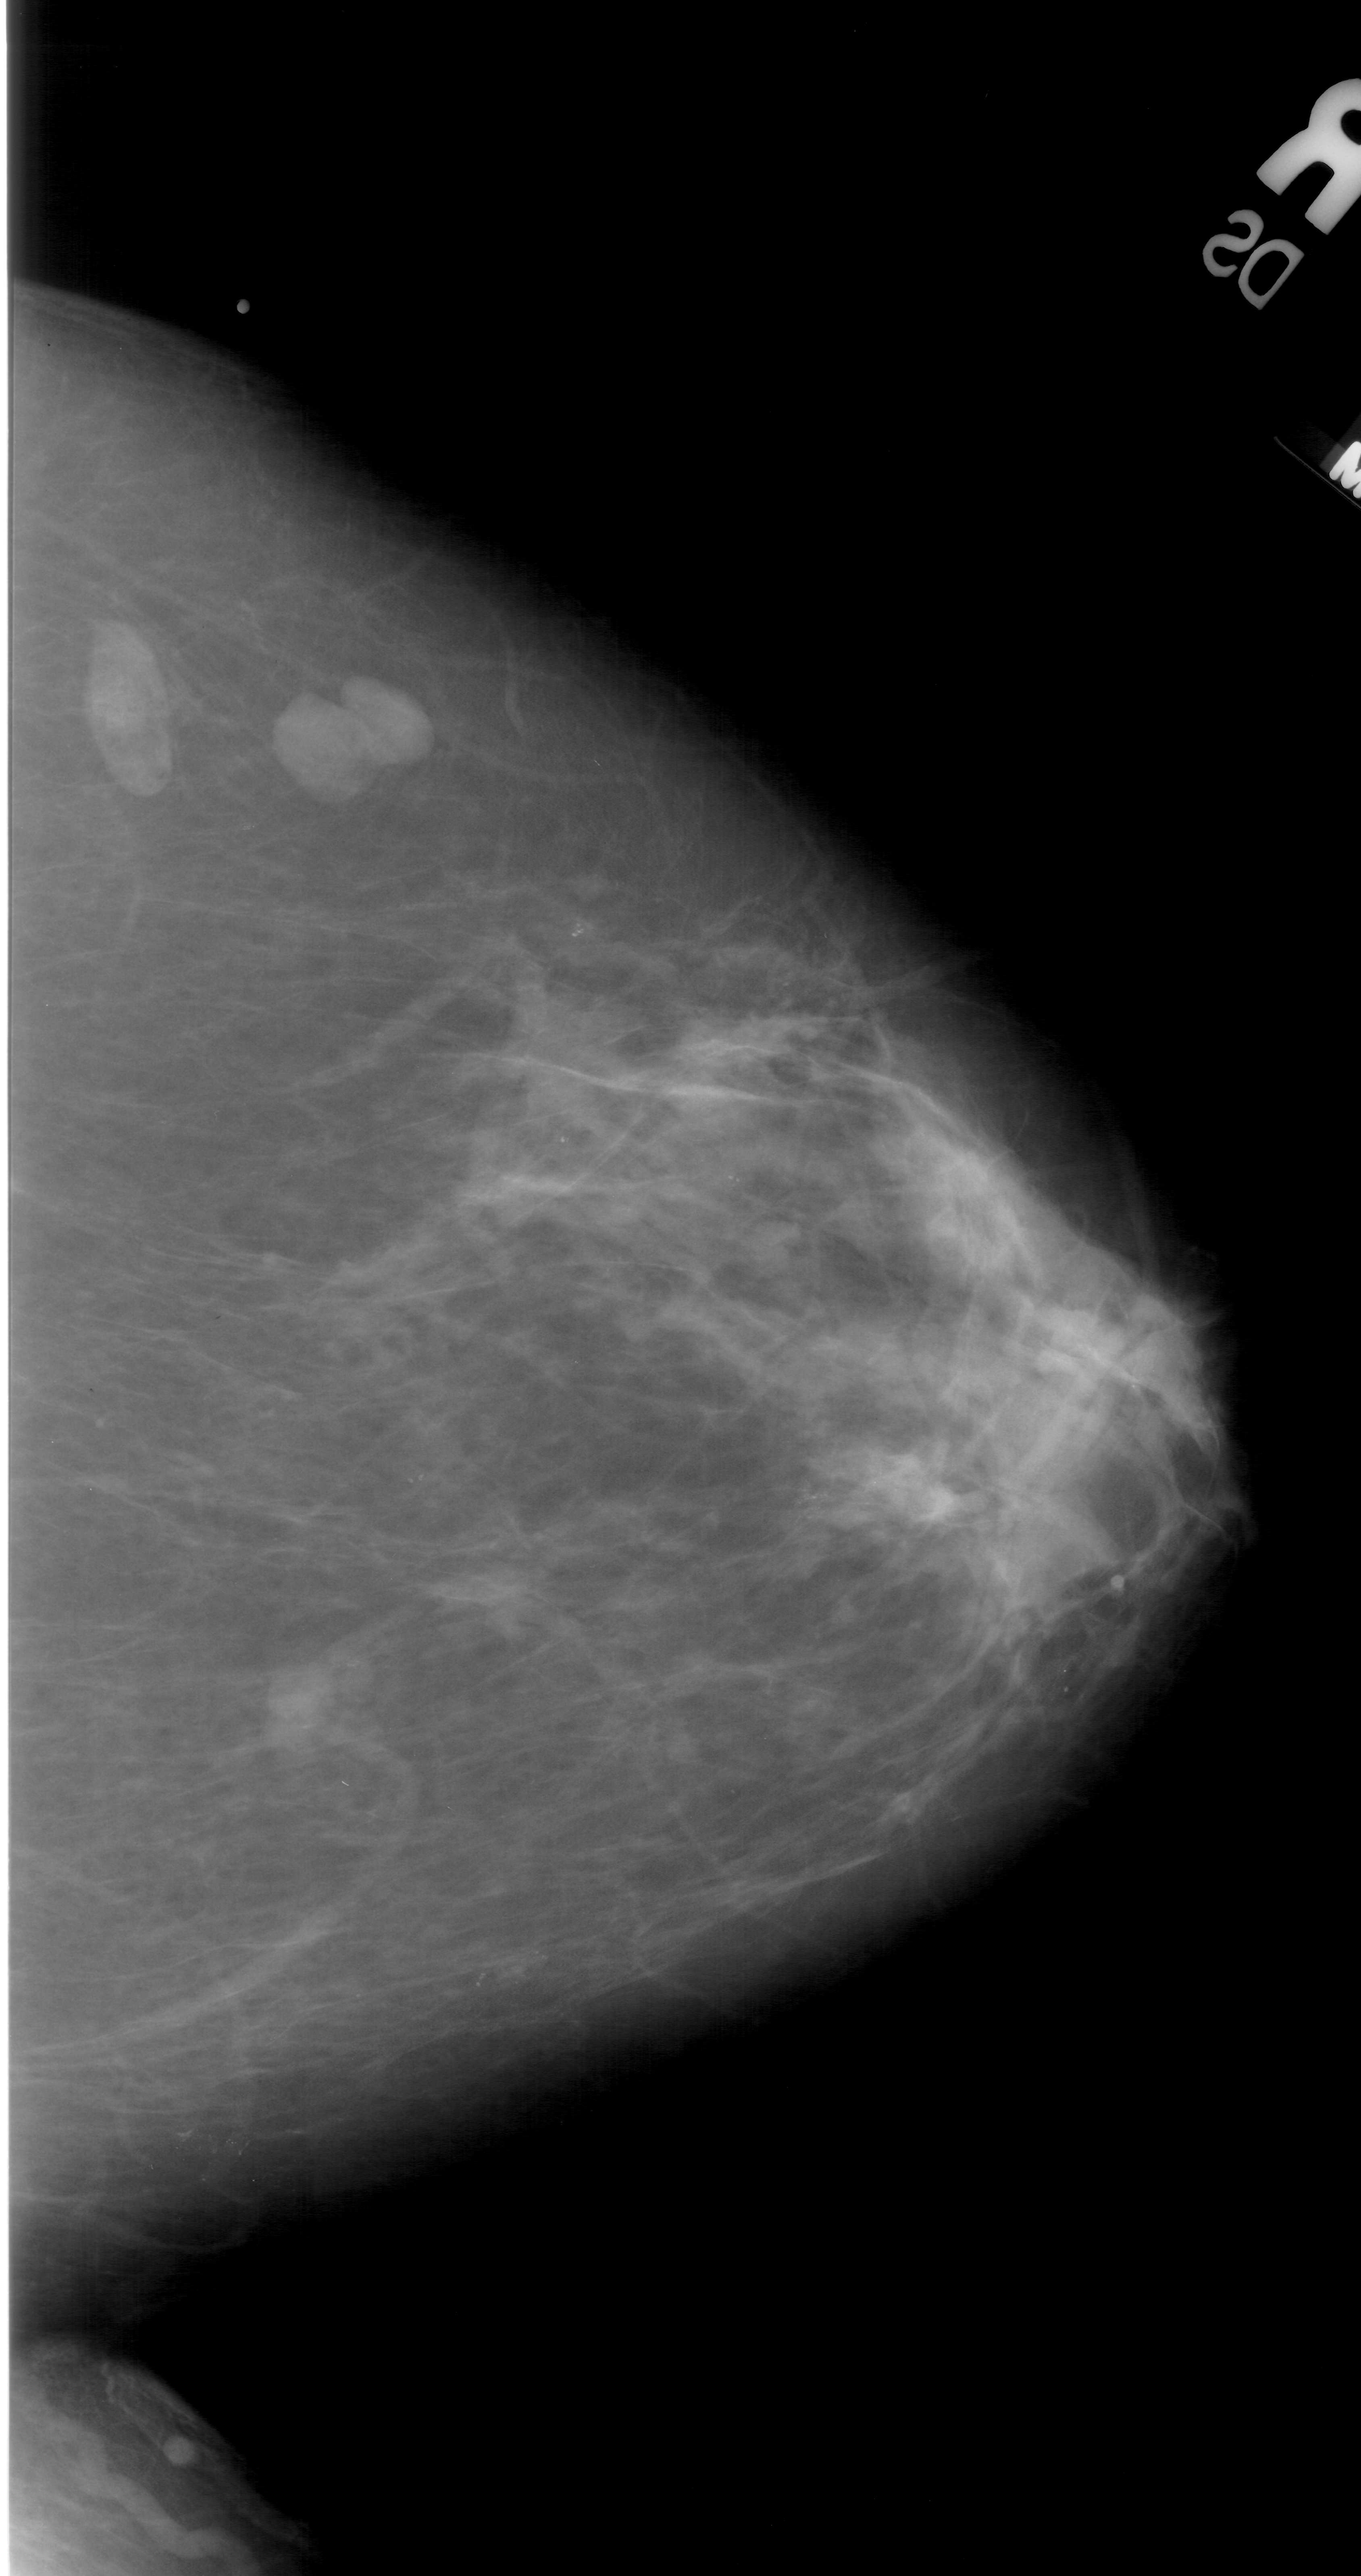
Scanned film-screen mammogram, right breast, CC view.
- Radiologist-marked abnormalities on this image: calcifications, morphology pleomorphic, distribution clustered; BI-RADS assessment category 3; pathology result (as recorded, not read from the image): benign.